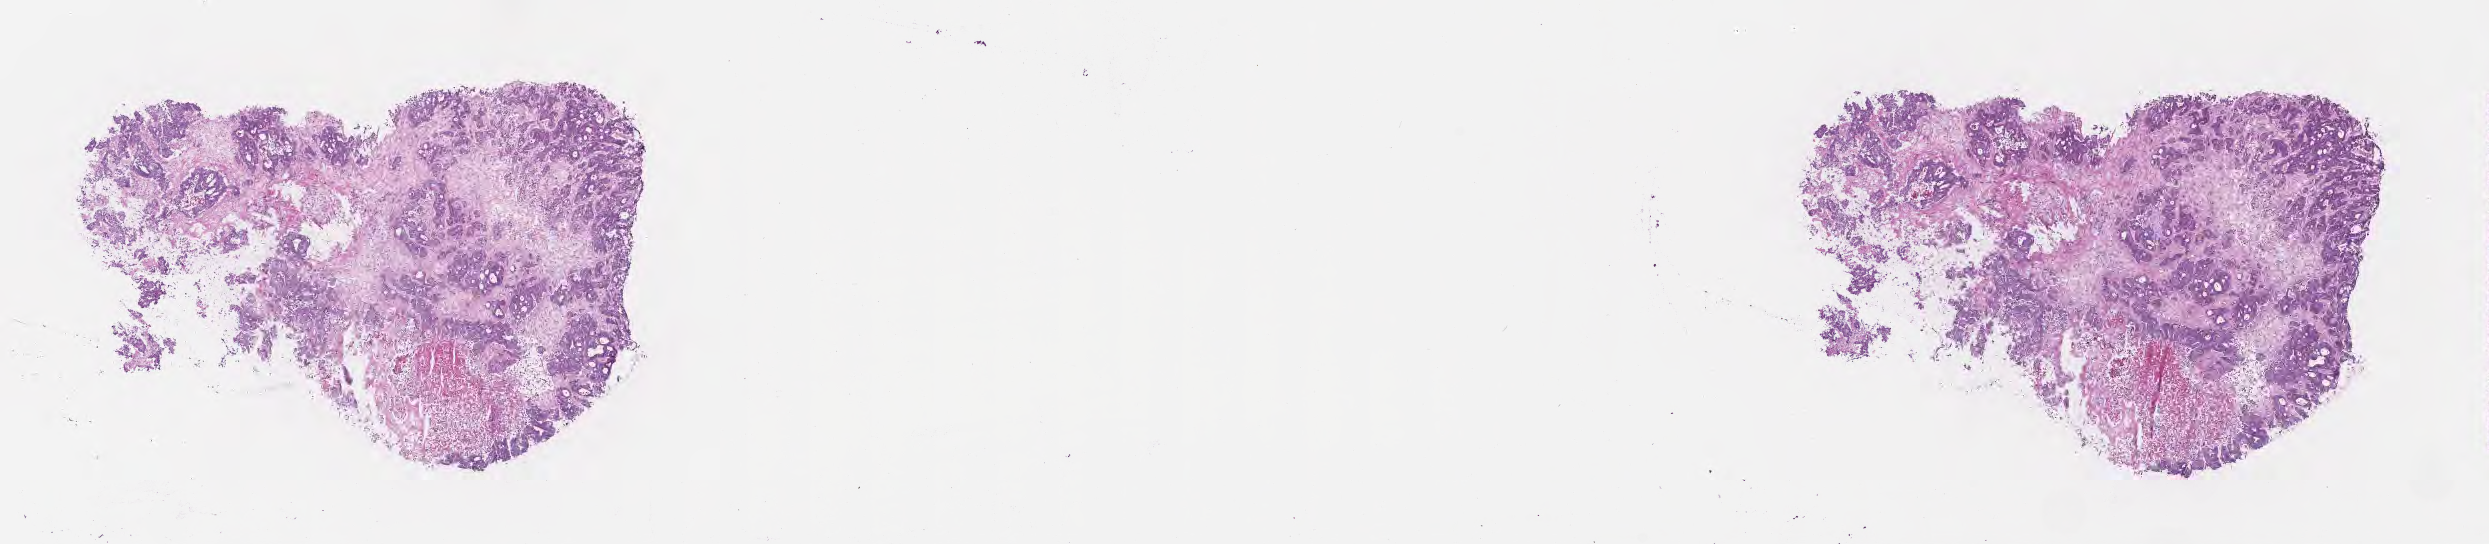
H&E whole-slide image — whole scanned area (about 20.1 x 4.4 mm) shown as a low-resolution overview. Frozen section (tissue freezing medium). Metastatic tumor tissue, resected from liver. Patient: male, age at initial diagnosis 63 years. Composition of this section per pathologist review: tumor cells 40%, tumor nuclei 85%, stromal cells 41%, necrosis 19%, normal cells 0%. Inflammatory infiltration, as recorded: lymphocyte infiltration 7%, monocyte infiltration 1%, neutrophil infiltration 0%.
Patient diagnosis (primary): Adenocarcinoma, NOS. Section: bottom of the tissue portion.